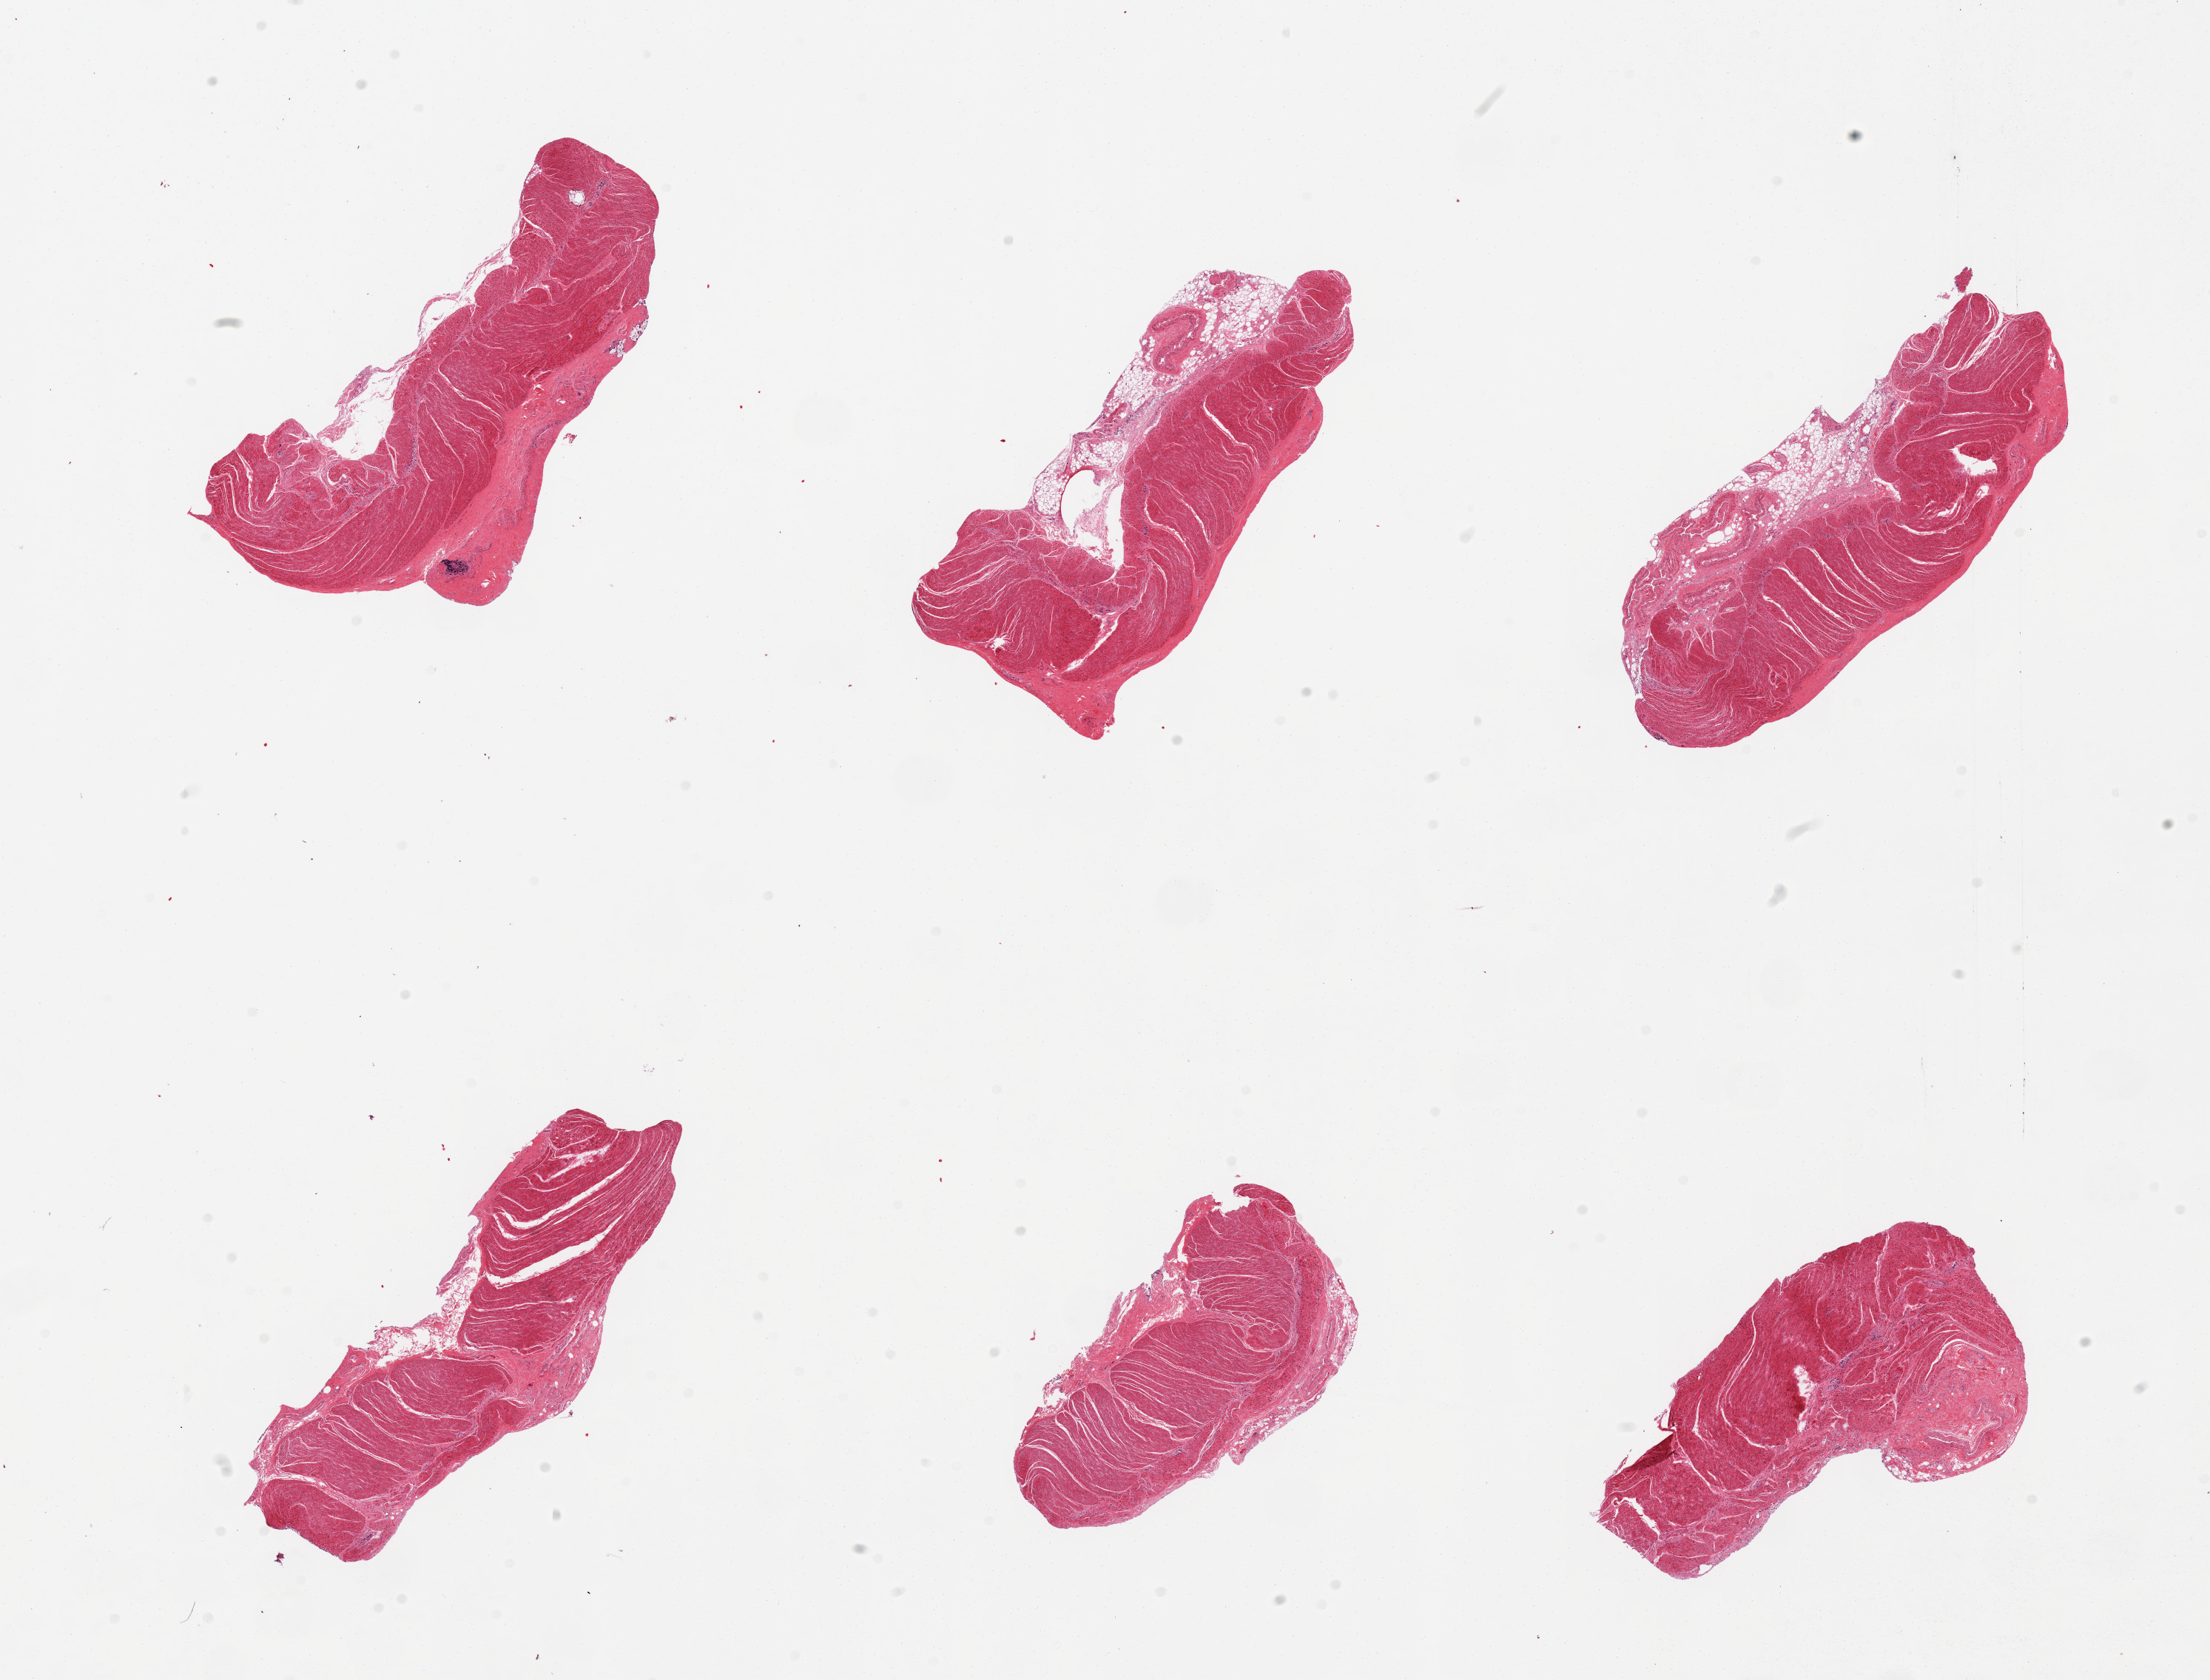
Whole-slide image, haematoxylin and eosin stain, low-resolution overview of the scanned area, about 23.6 x 18.0 mm. PAXgene-fixed paraffin-embedded (PFPE) section. Sampled site (target tissue): sigmoid colon. Donor tissue sample. Donor sex: male.
Pathologist's review note for this sample: 6 pieces, muscularis, attached fat and vessels.